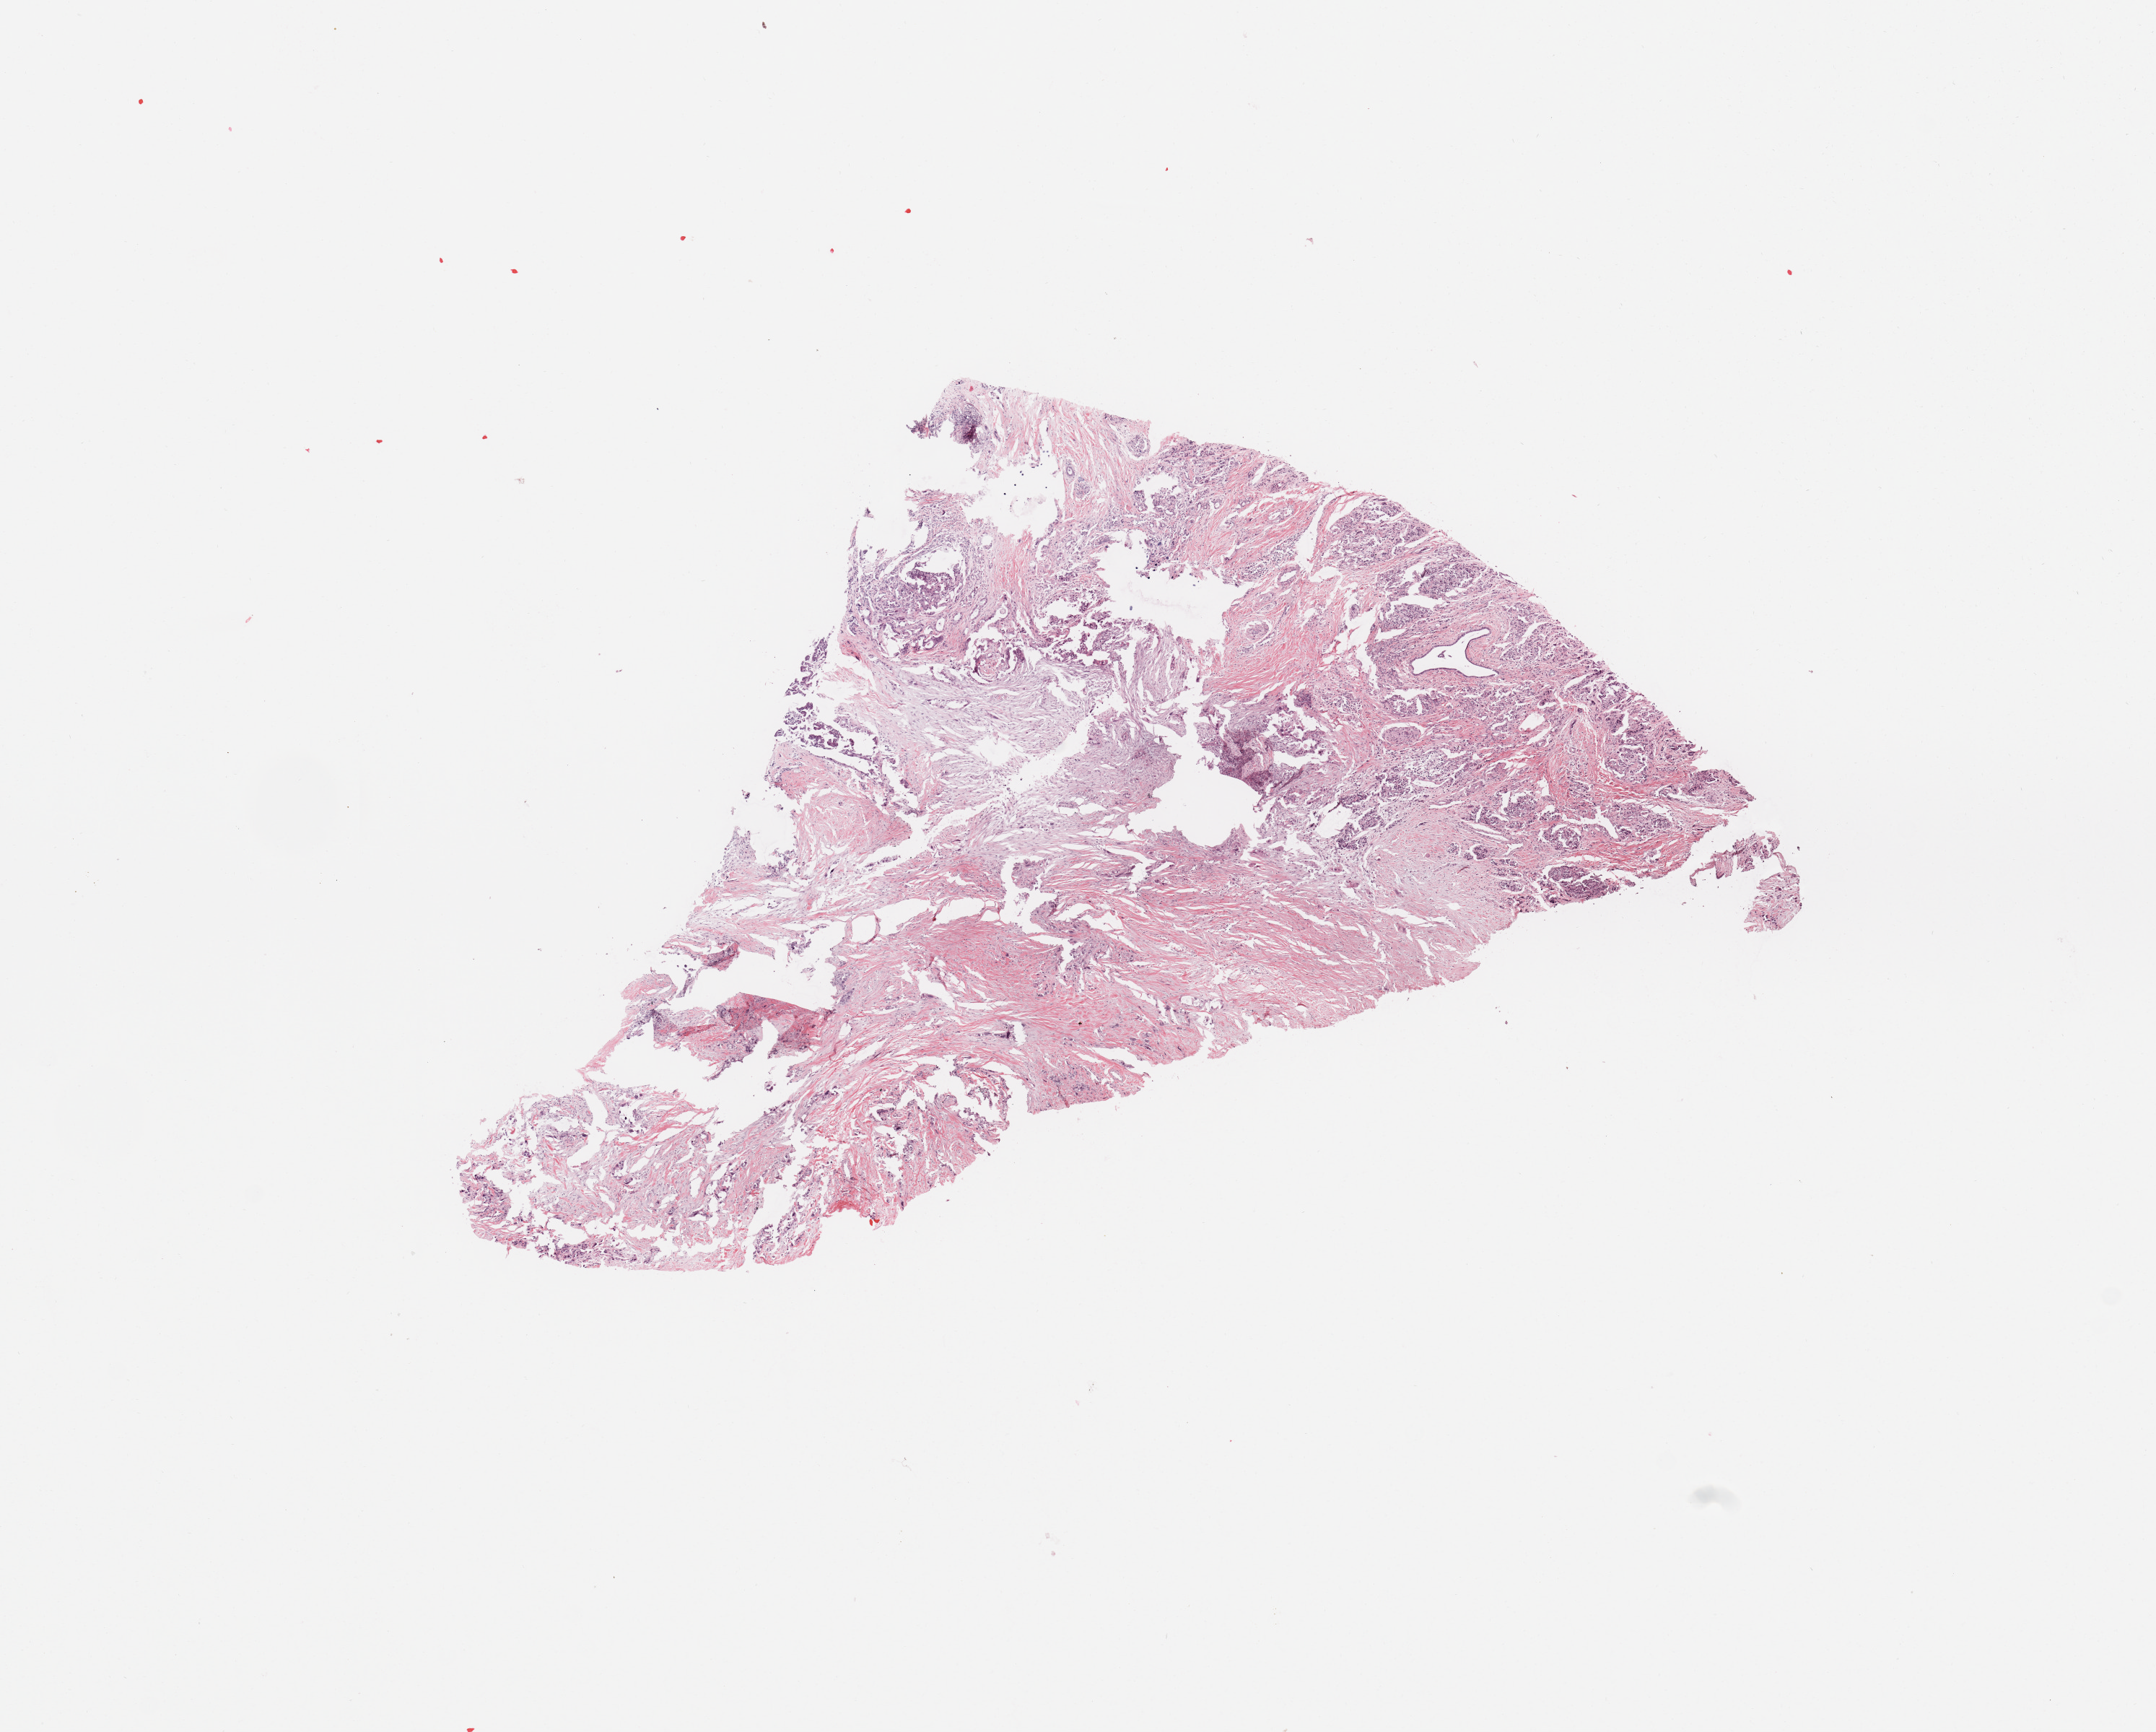
Whole-slide histology image, H&E, a low-resolution overview of the entire scanned area, about 11.8 x 9.5 mm (acquisition: 20x scan); tumour tissue sample, sampled site: pancreas. Patient: female, age 49 years. Histologic grade: G2 (moderately differentiated). Slide review estimates, as recorded: tumour nuclei 30%, necrosis 0%.
AJCC pathologic stage: III. Primary tumour site (as recorded): head. Diagnosis: Infiltrating duct carcinoma, NOS.